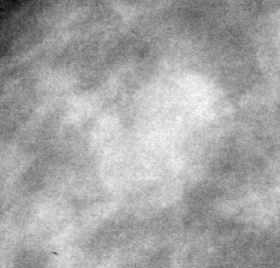
Cropped region of a digitized screen-film mammogram centred on a radiologist-marked abnormality; right breast; CC view; BI-RADS breast density category 2 (scale 1–4).
Marked abnormality: mass, shape lobulated, margins circumscribed; BI-RADS assessment category 3; subtlety rating 5 on a 1 (subtle) to 5 (obvious) scale; pathology (as recorded): benign.